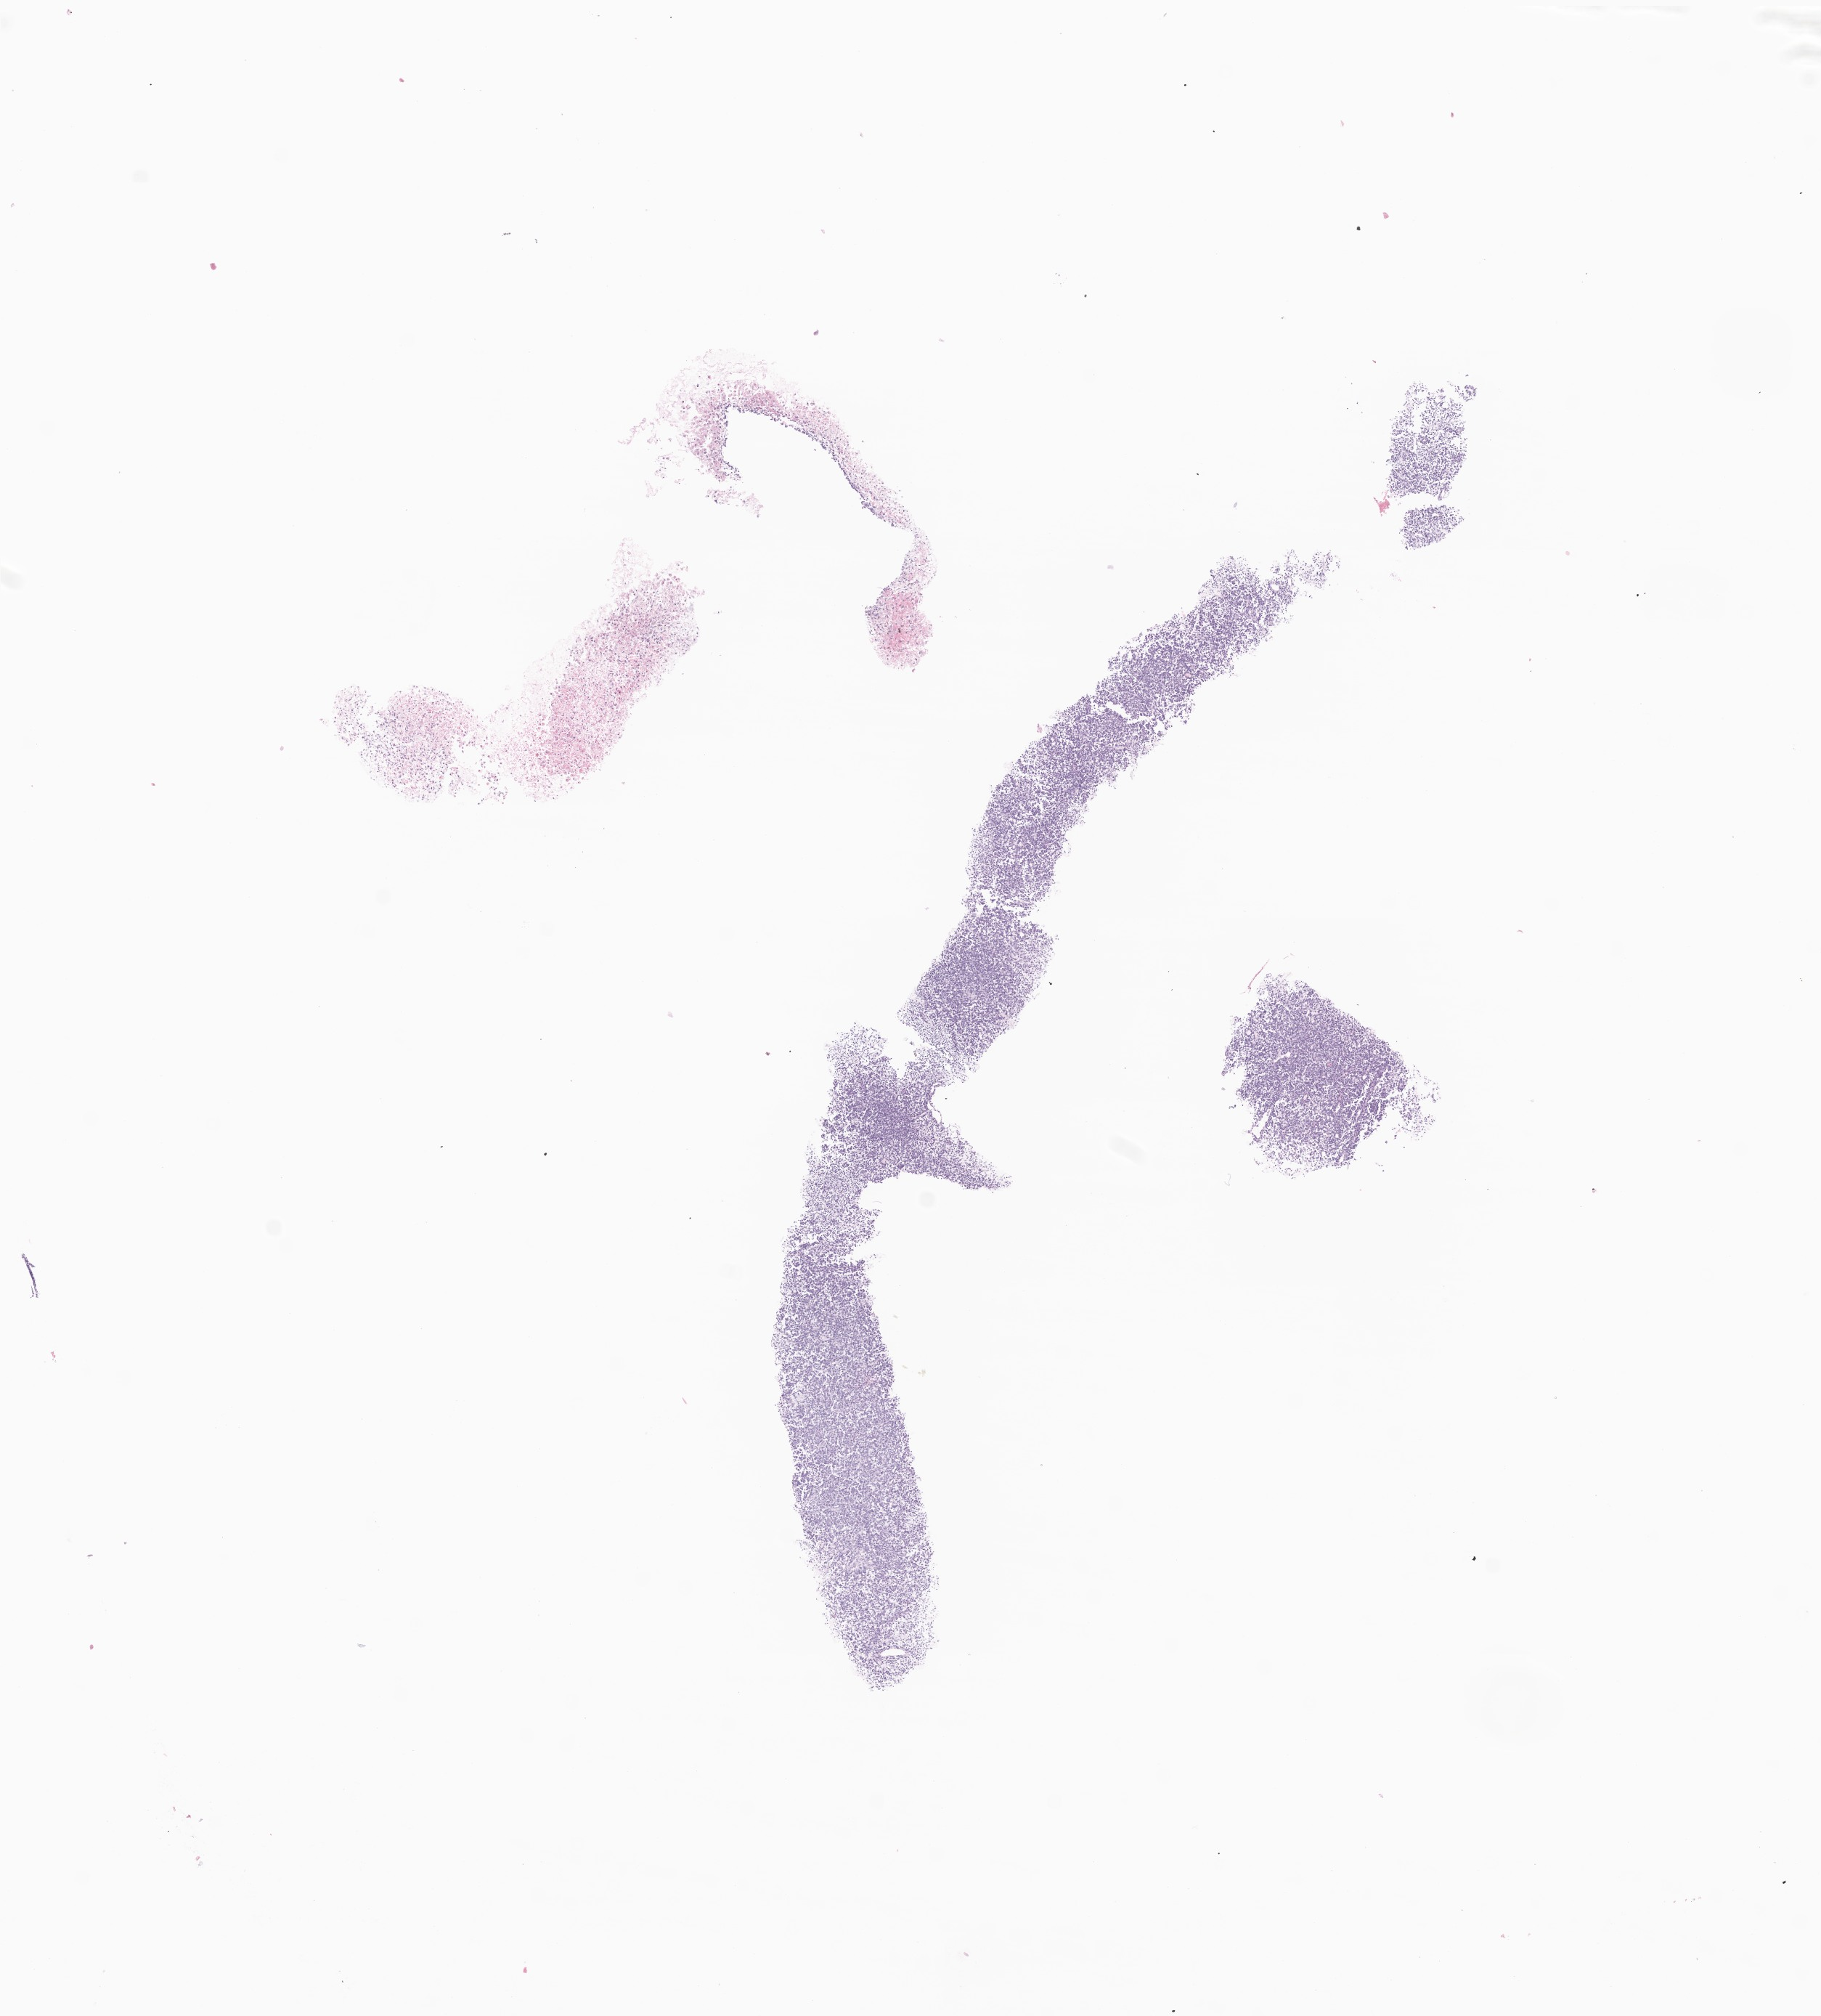
H&E whole-slide image of tumor tissue from the soft tissue of upper extremity — a low-resolution overview of the entire scanned area, about 10.6 x 11.7 mm; FFPE section. Male patient, age 179 months.
Diagnosis (ICD-O-3 morphology term): Undifferentiated sarcoma.